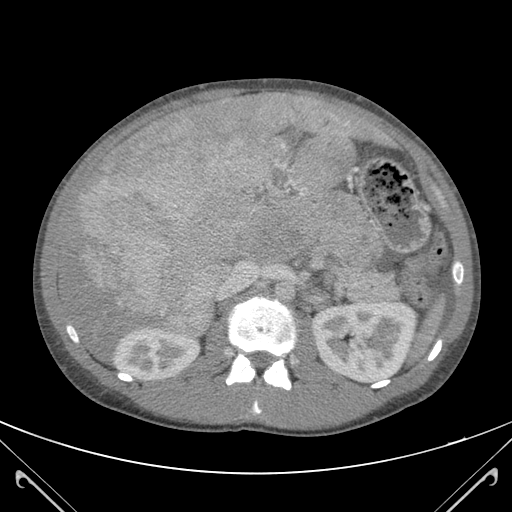
Contrast-enhanced abdominal CT (liver protocol), one axial slice. Position 67 of 118 along the scan axis. Soft-tissue window (W 400 / L 40 HU). 3 mm slice thickness. 512 × 512 image matrix. Case-level facts recorded for this patient, not image findings: diagnosis: hepatocellular carcinoma (patient treated with transarterial chemoembolisation; whether this scan precedes or follows treatment is not stated here); TNM stage (as recorded): Stage-IIIB; Child-Pugh class: A; tumour nodularity: uninodular.
Annotated regions visible in this slice (semi-automatic segmentation, software-assisted and operator-edited):
- abdominal aorta: bounding box (x1, y1, x2, y2) in pixels: (274, 279, 296, 302)
- liver parenchyma outside the tumour (the mass and vessels are separate outlines, so this box may not span the whole liver): (59, 93, 369, 357)
- mass: (62, 94, 366, 335)
- liver vessels: (218, 205, 315, 300)